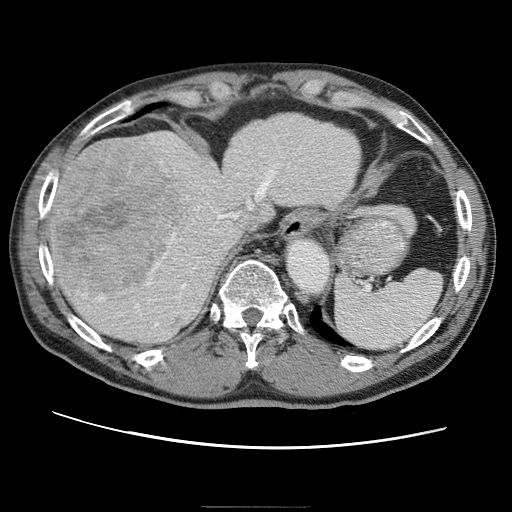
Contrast-enhanced abdominal CT (liver protocol), one axial slice; slice 50 of 75 in the series (ordered by position); reconstruction kernel STANDARD; one of 2 acquisitions stored at this slice position; soft-tissue window (W 400 / L 40 HU); 512 × 512 image matrix, field of view 360 × 360 mm. From the clinical record (not read from this slice): diagnosis: hepatocellular carcinoma (patient treated with transarterial chemoembolisation; whether this scan precedes or follows treatment is not stated here); TNM stage (as recorded): Stage-II; Child-Pugh class: A; tumour differentiation: well differentiated; tumour nodularity: multinodular.
Outlined on this slice (semi-automatic segmentation, software-assisted and operator-edited):
- abdominal aorta: box from (x=285, y=239) to (x=327, y=292) px
- liver parenchyma outside the tumour (the mass and vessels are separate outlines, so this box may not span the whole liver): (x=50, y=114)–(x=364, y=342)
- mass: (x=52, y=142)–(x=188, y=302)
- liver vessels: (x=63, y=152)–(x=303, y=308)